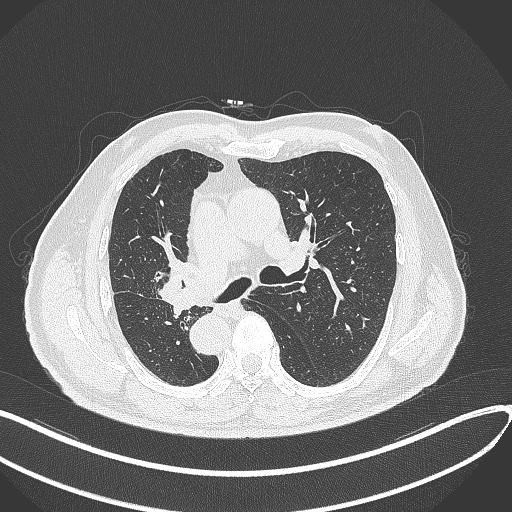
Chest CT, one axial slice. Lung window (W 1500 / L -600 HU). 512 × 512 image matrix. Male patient, age 67 years. From the clinical record (not read from this slice): clinical TNM (as recorded): T2a N0 M0.
Outlined on this slice (rectangle marked by the reading radiologist):
- lung tumour (recorded histology: squamous cell carcinoma): bounding box <158,257,199,312> (left, top, right, bottom; pixels)